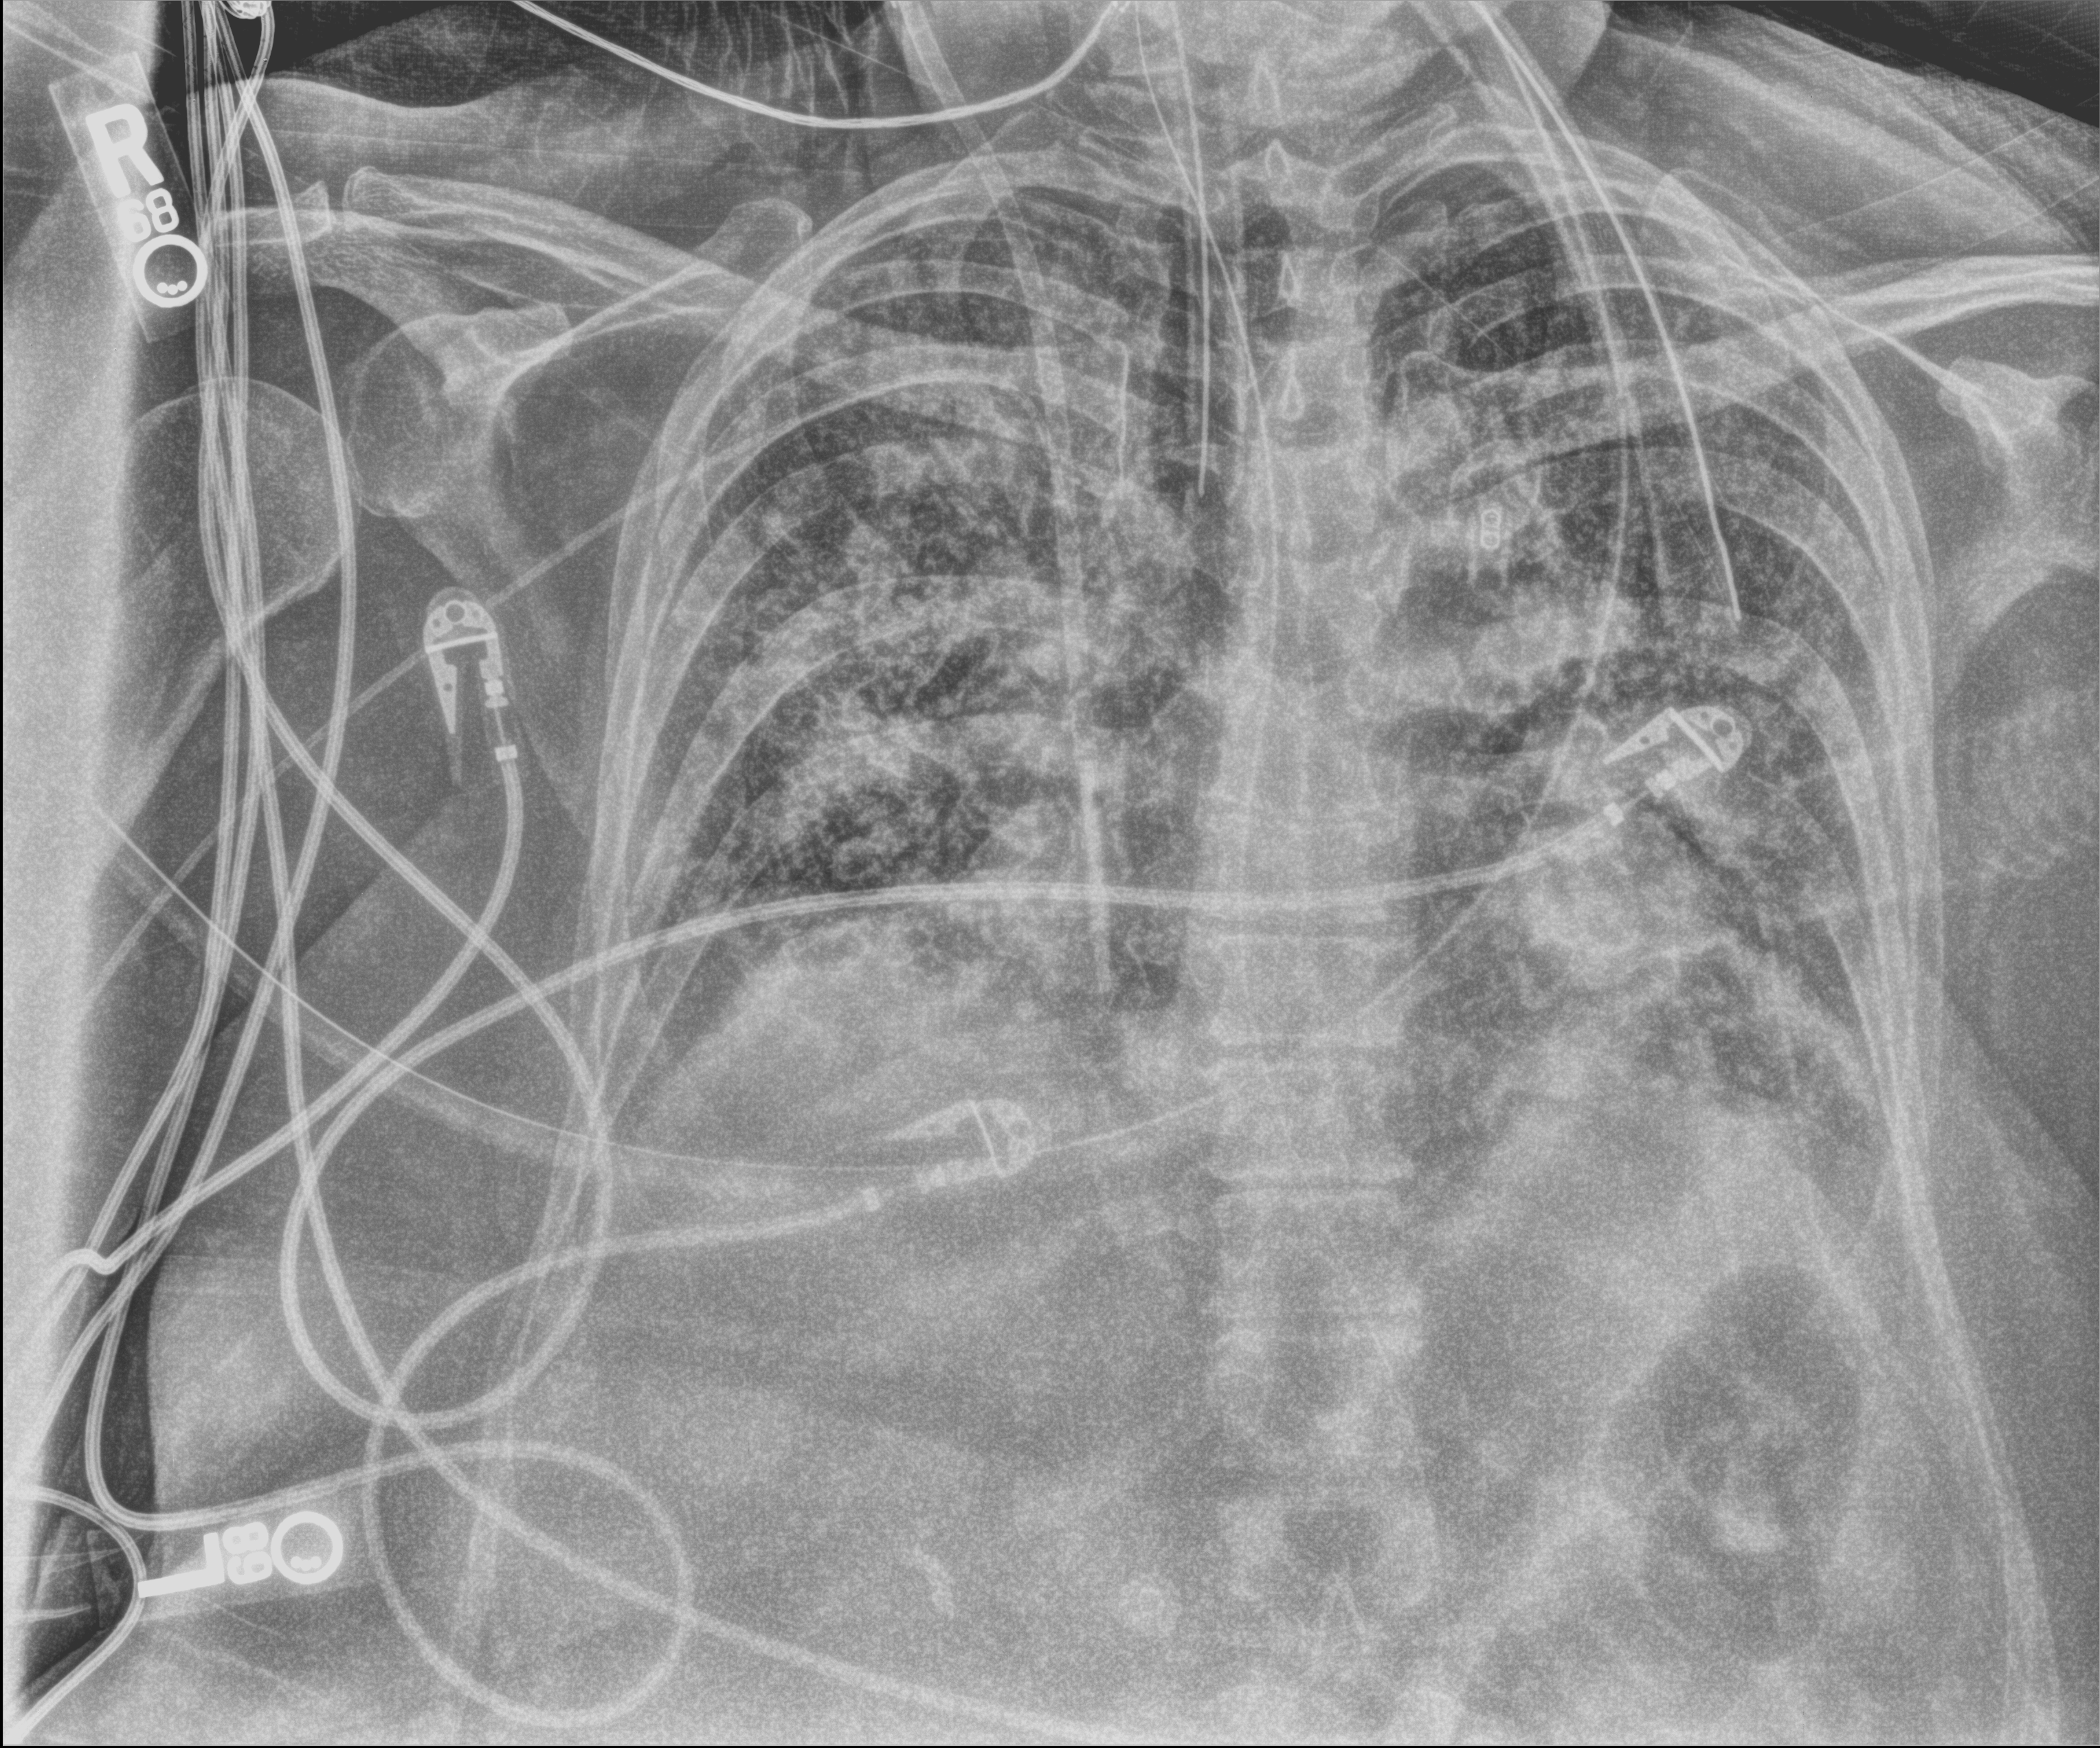
Bedside chest radiograph (computed radiography); anteroposterior (AP) projection. Patient hospitalised with COVID-19; female, aged 60–74 years.
From the hospital-stay record, not from the radiograph (when in the stay this image was taken is not recorded): length of hospital stay: 45 days; mechanically ventilated during this hospital stay: yes.